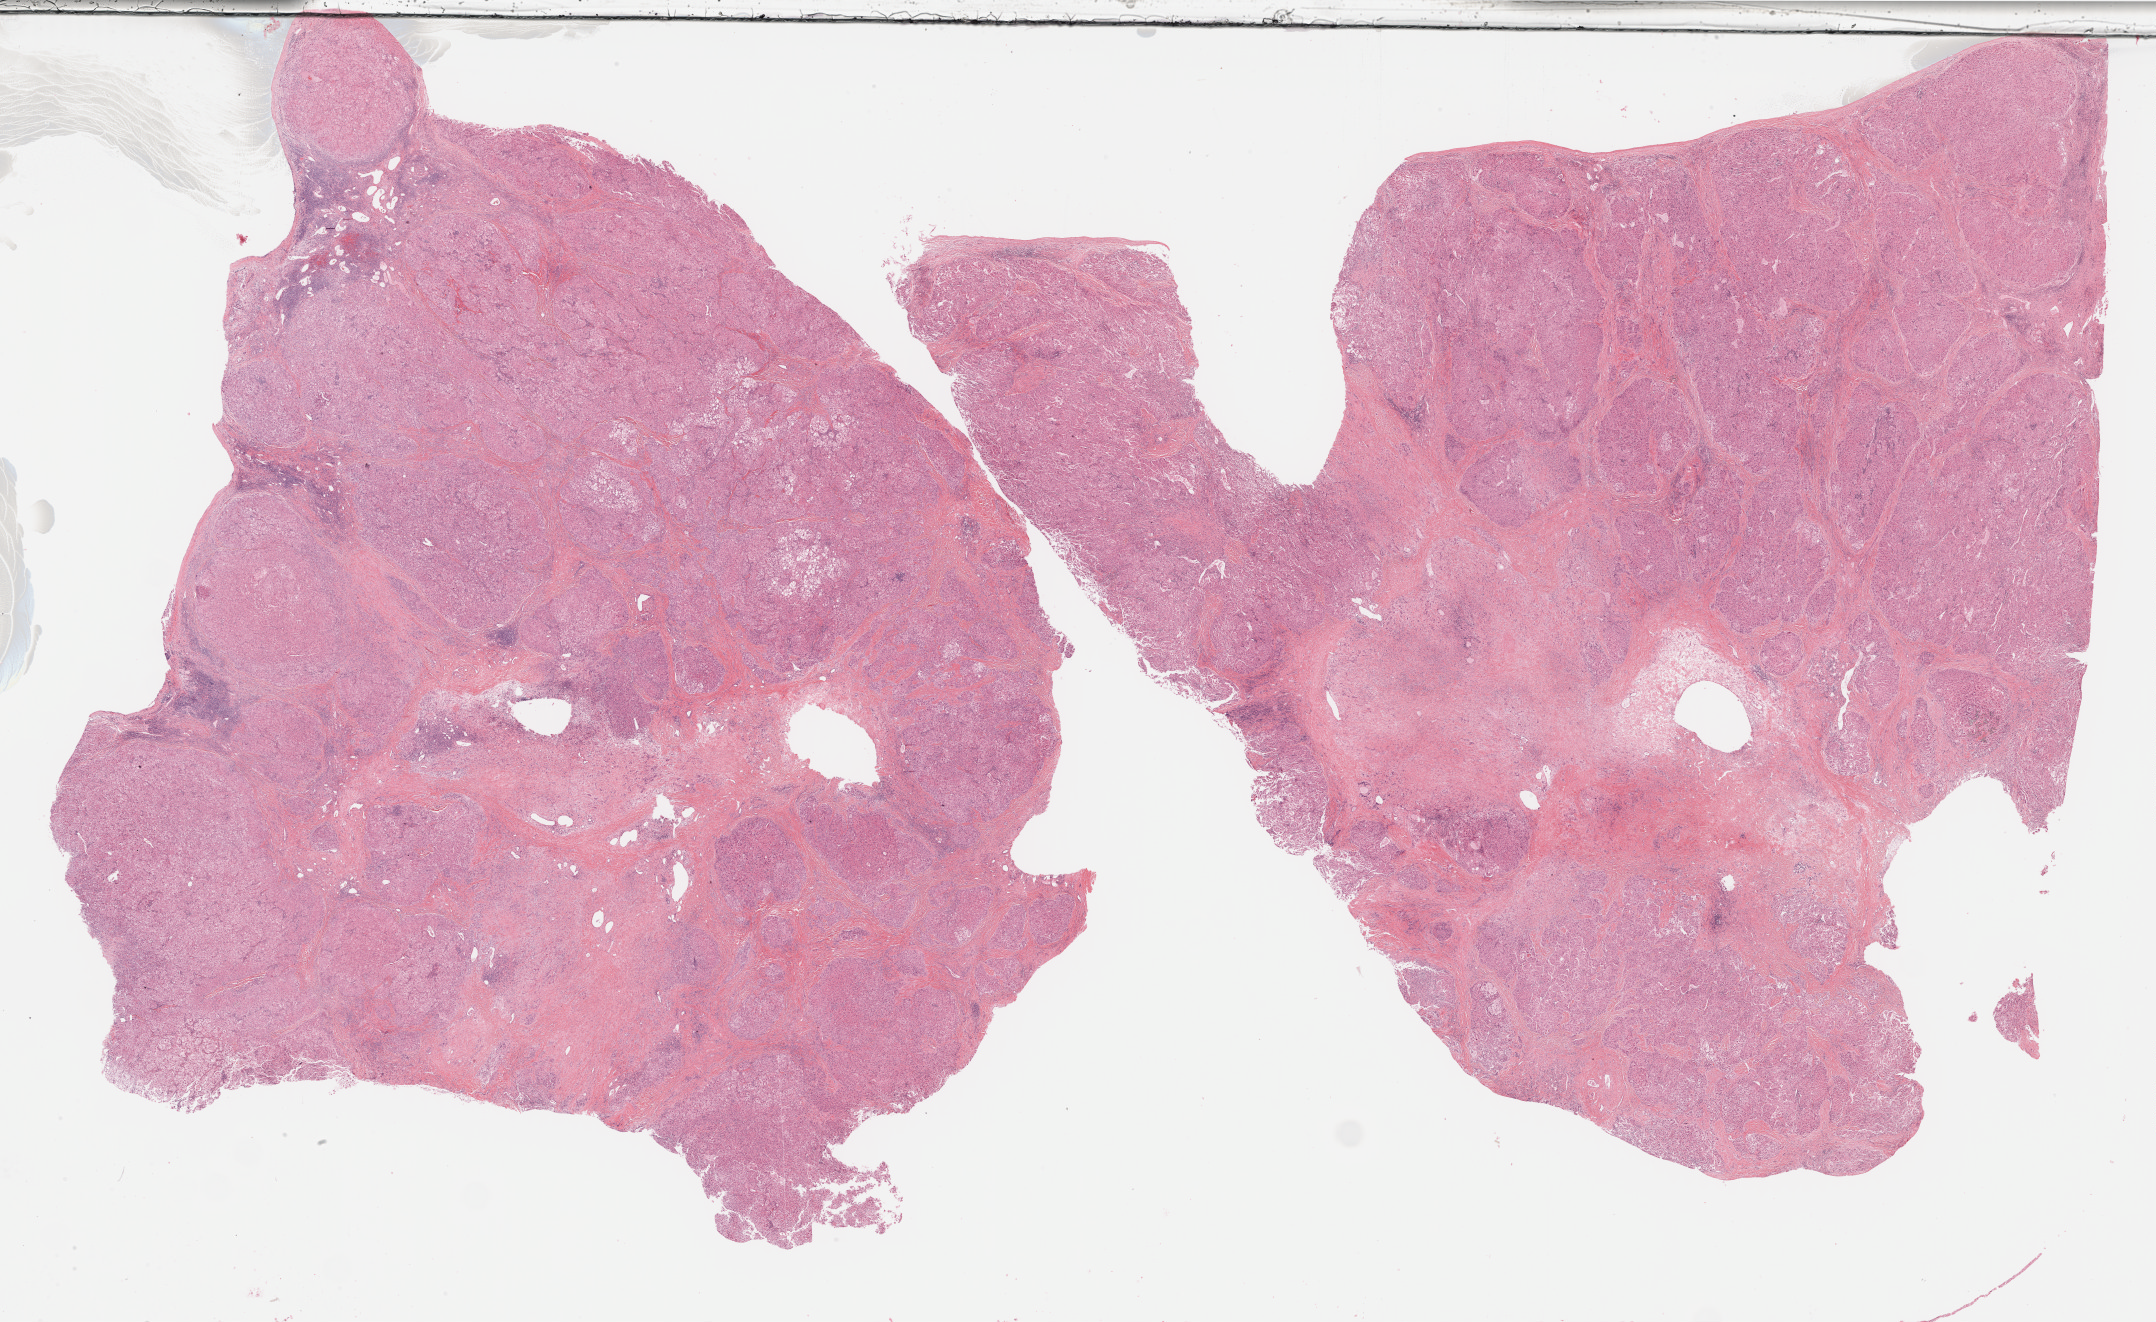
Hematoxylin and eosin (H&E) stained whole-slide image, whole scanned area (about 34.9 x 21.4 mm, from a 40x scan) shown as a low-resolution overview. Formalin-fixed paraffin-embedded (FFPE) diagnostic section. Liver, primary tumour sample. Male patient; age at initial diagnosis 68 years. Histologic grade: G3 (poorly differentiated).
AJCC pathologic stage: IIIA (5th edition). Histologic diagnosis: Hepatocellular carcinoma, NOS.